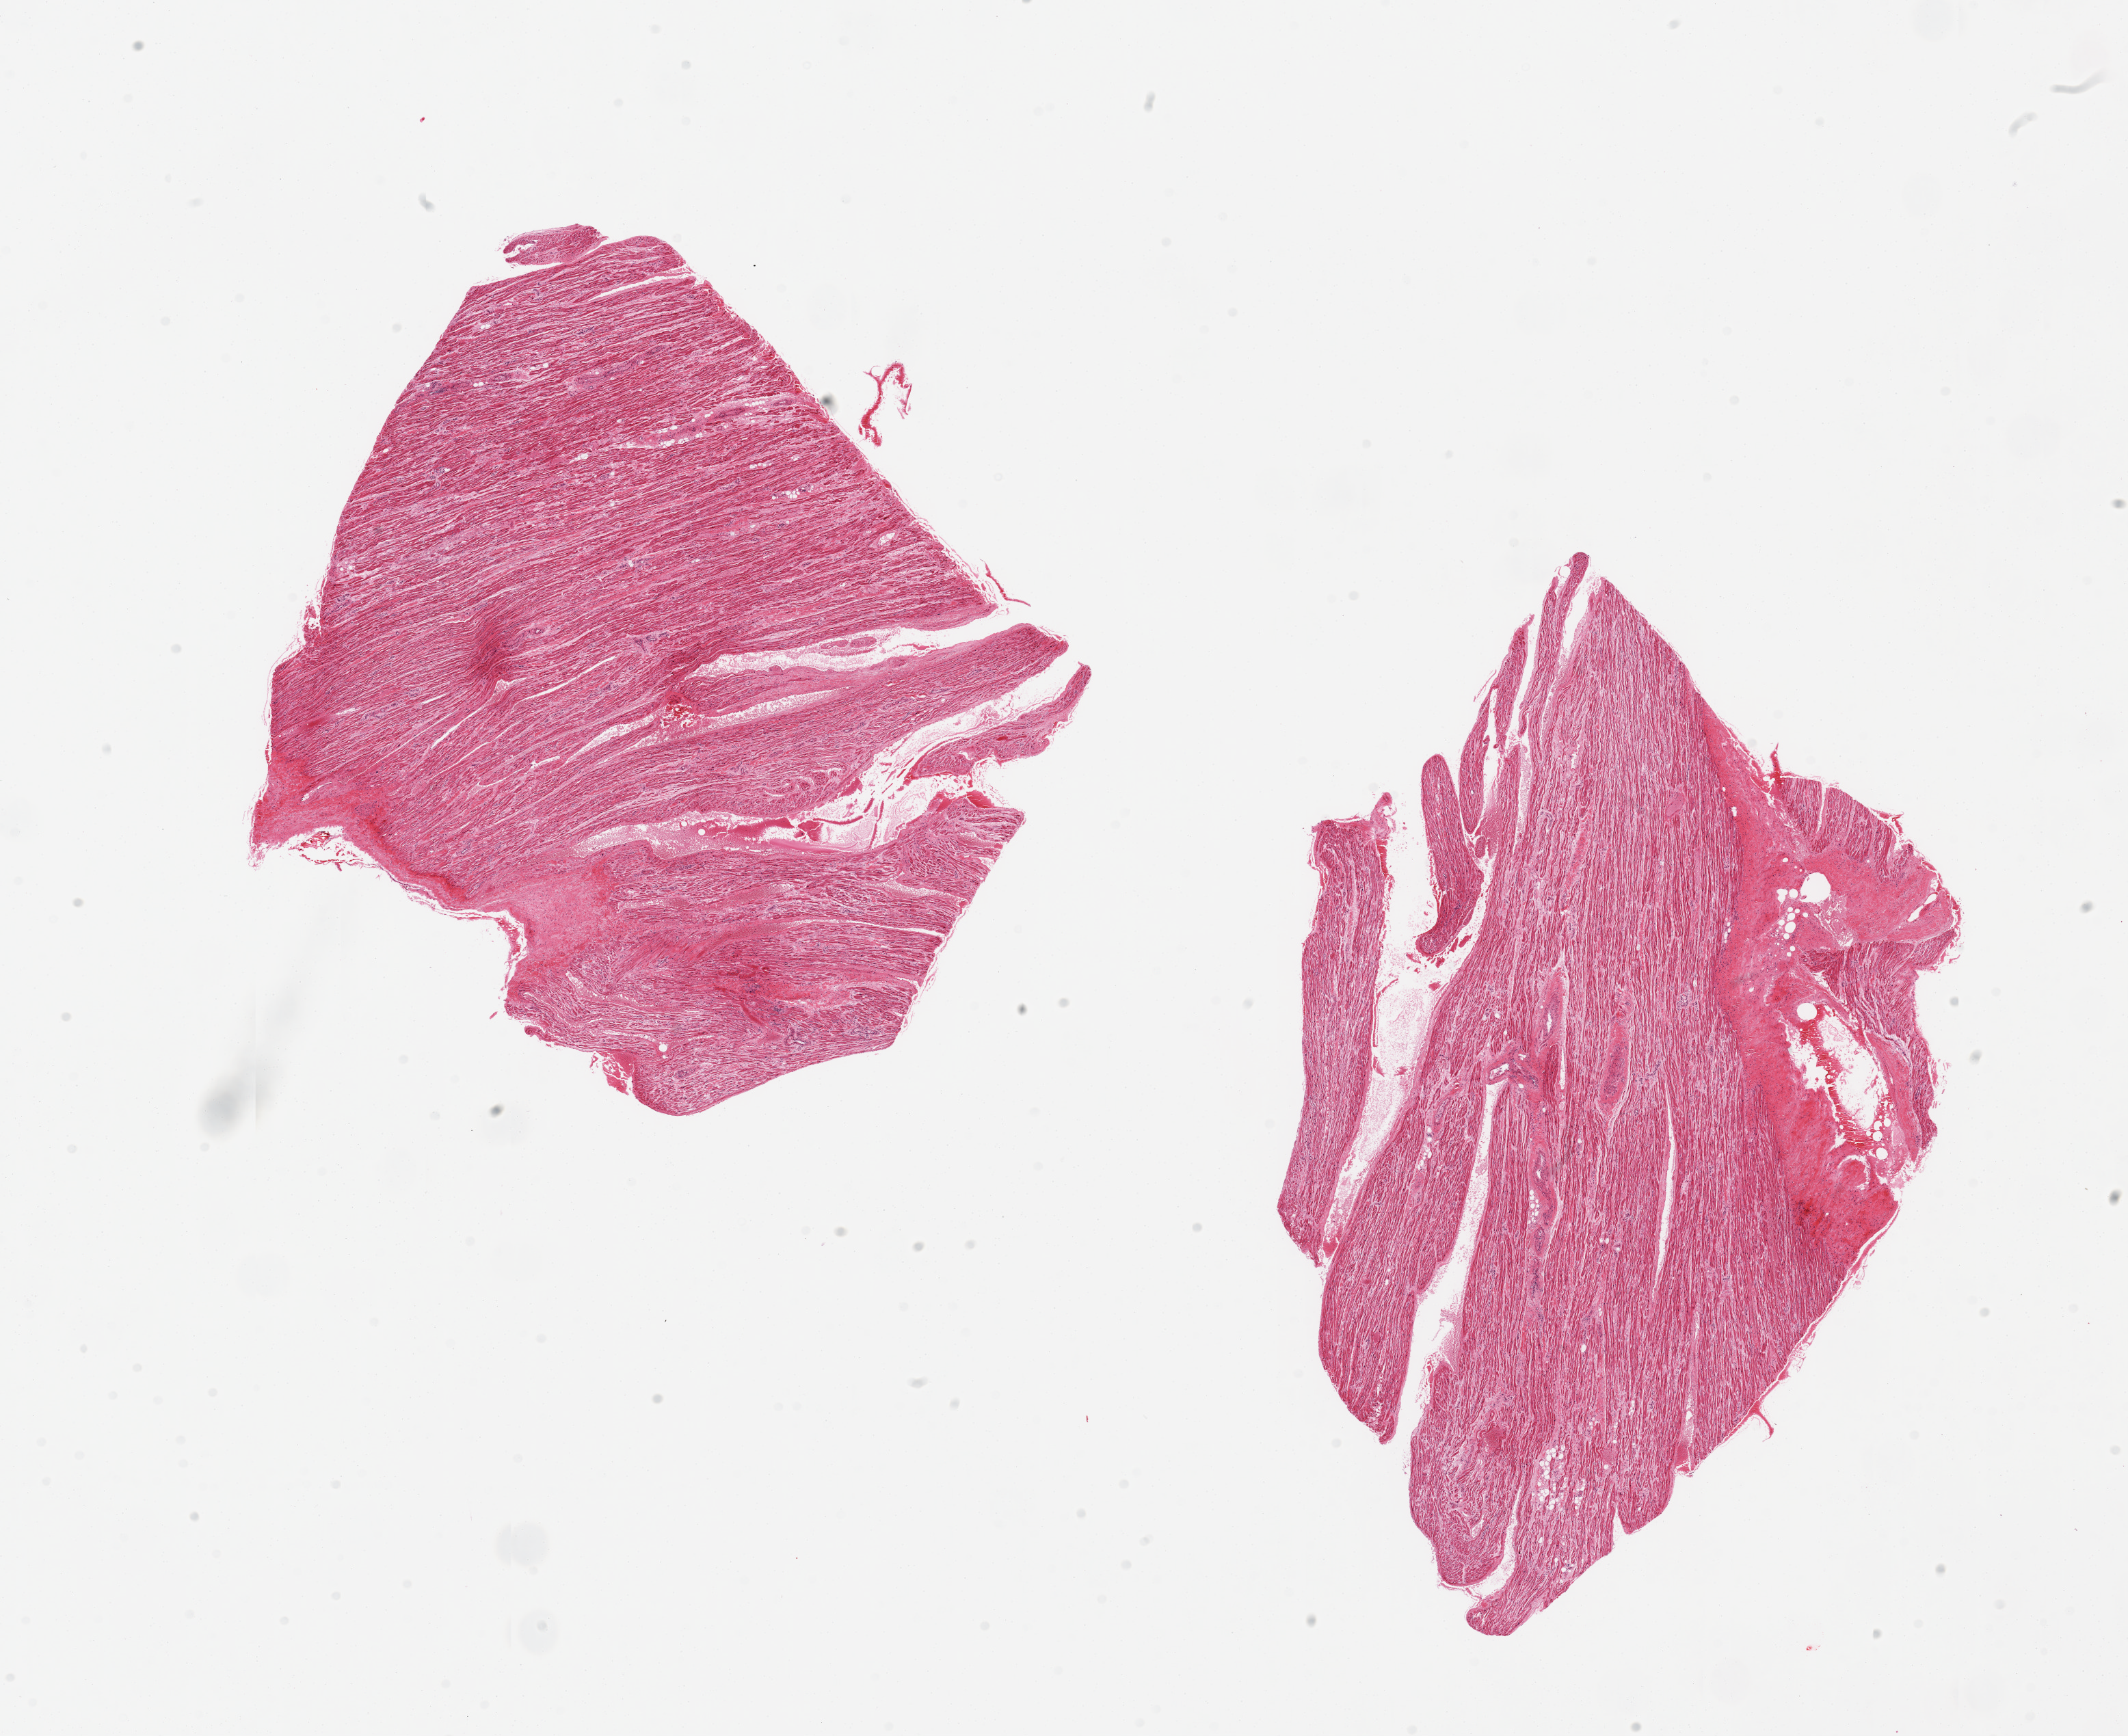
Haematoxylin and eosin whole-slide image, low-resolution overview of the scanned area, about 24.6 x 20.1 mm (slide scanned at 20x), PAXgene-fixed, paraffin-embedded tissue, target tissue: auricular appendage, tissue donor sample. Donor: male.
Review note (as recorded): 2 pieces, no abnormalities.